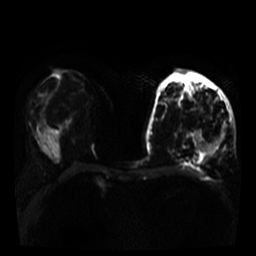
Breast MRI, one axial slice. Position 17 of 35 along the scan axis. Diffusion-weighted series; image 2 of 4 stored at this slice position (different b-values; order by instance number). 3 T. 5 mm slice thickness. 256 × 256 image matrix. Female patient.
Outlined on this slice (outlined manually by an expert reader):
- tumour on diffusion-weighted imaging: box from (x=197, y=131) to (x=224, y=154) px